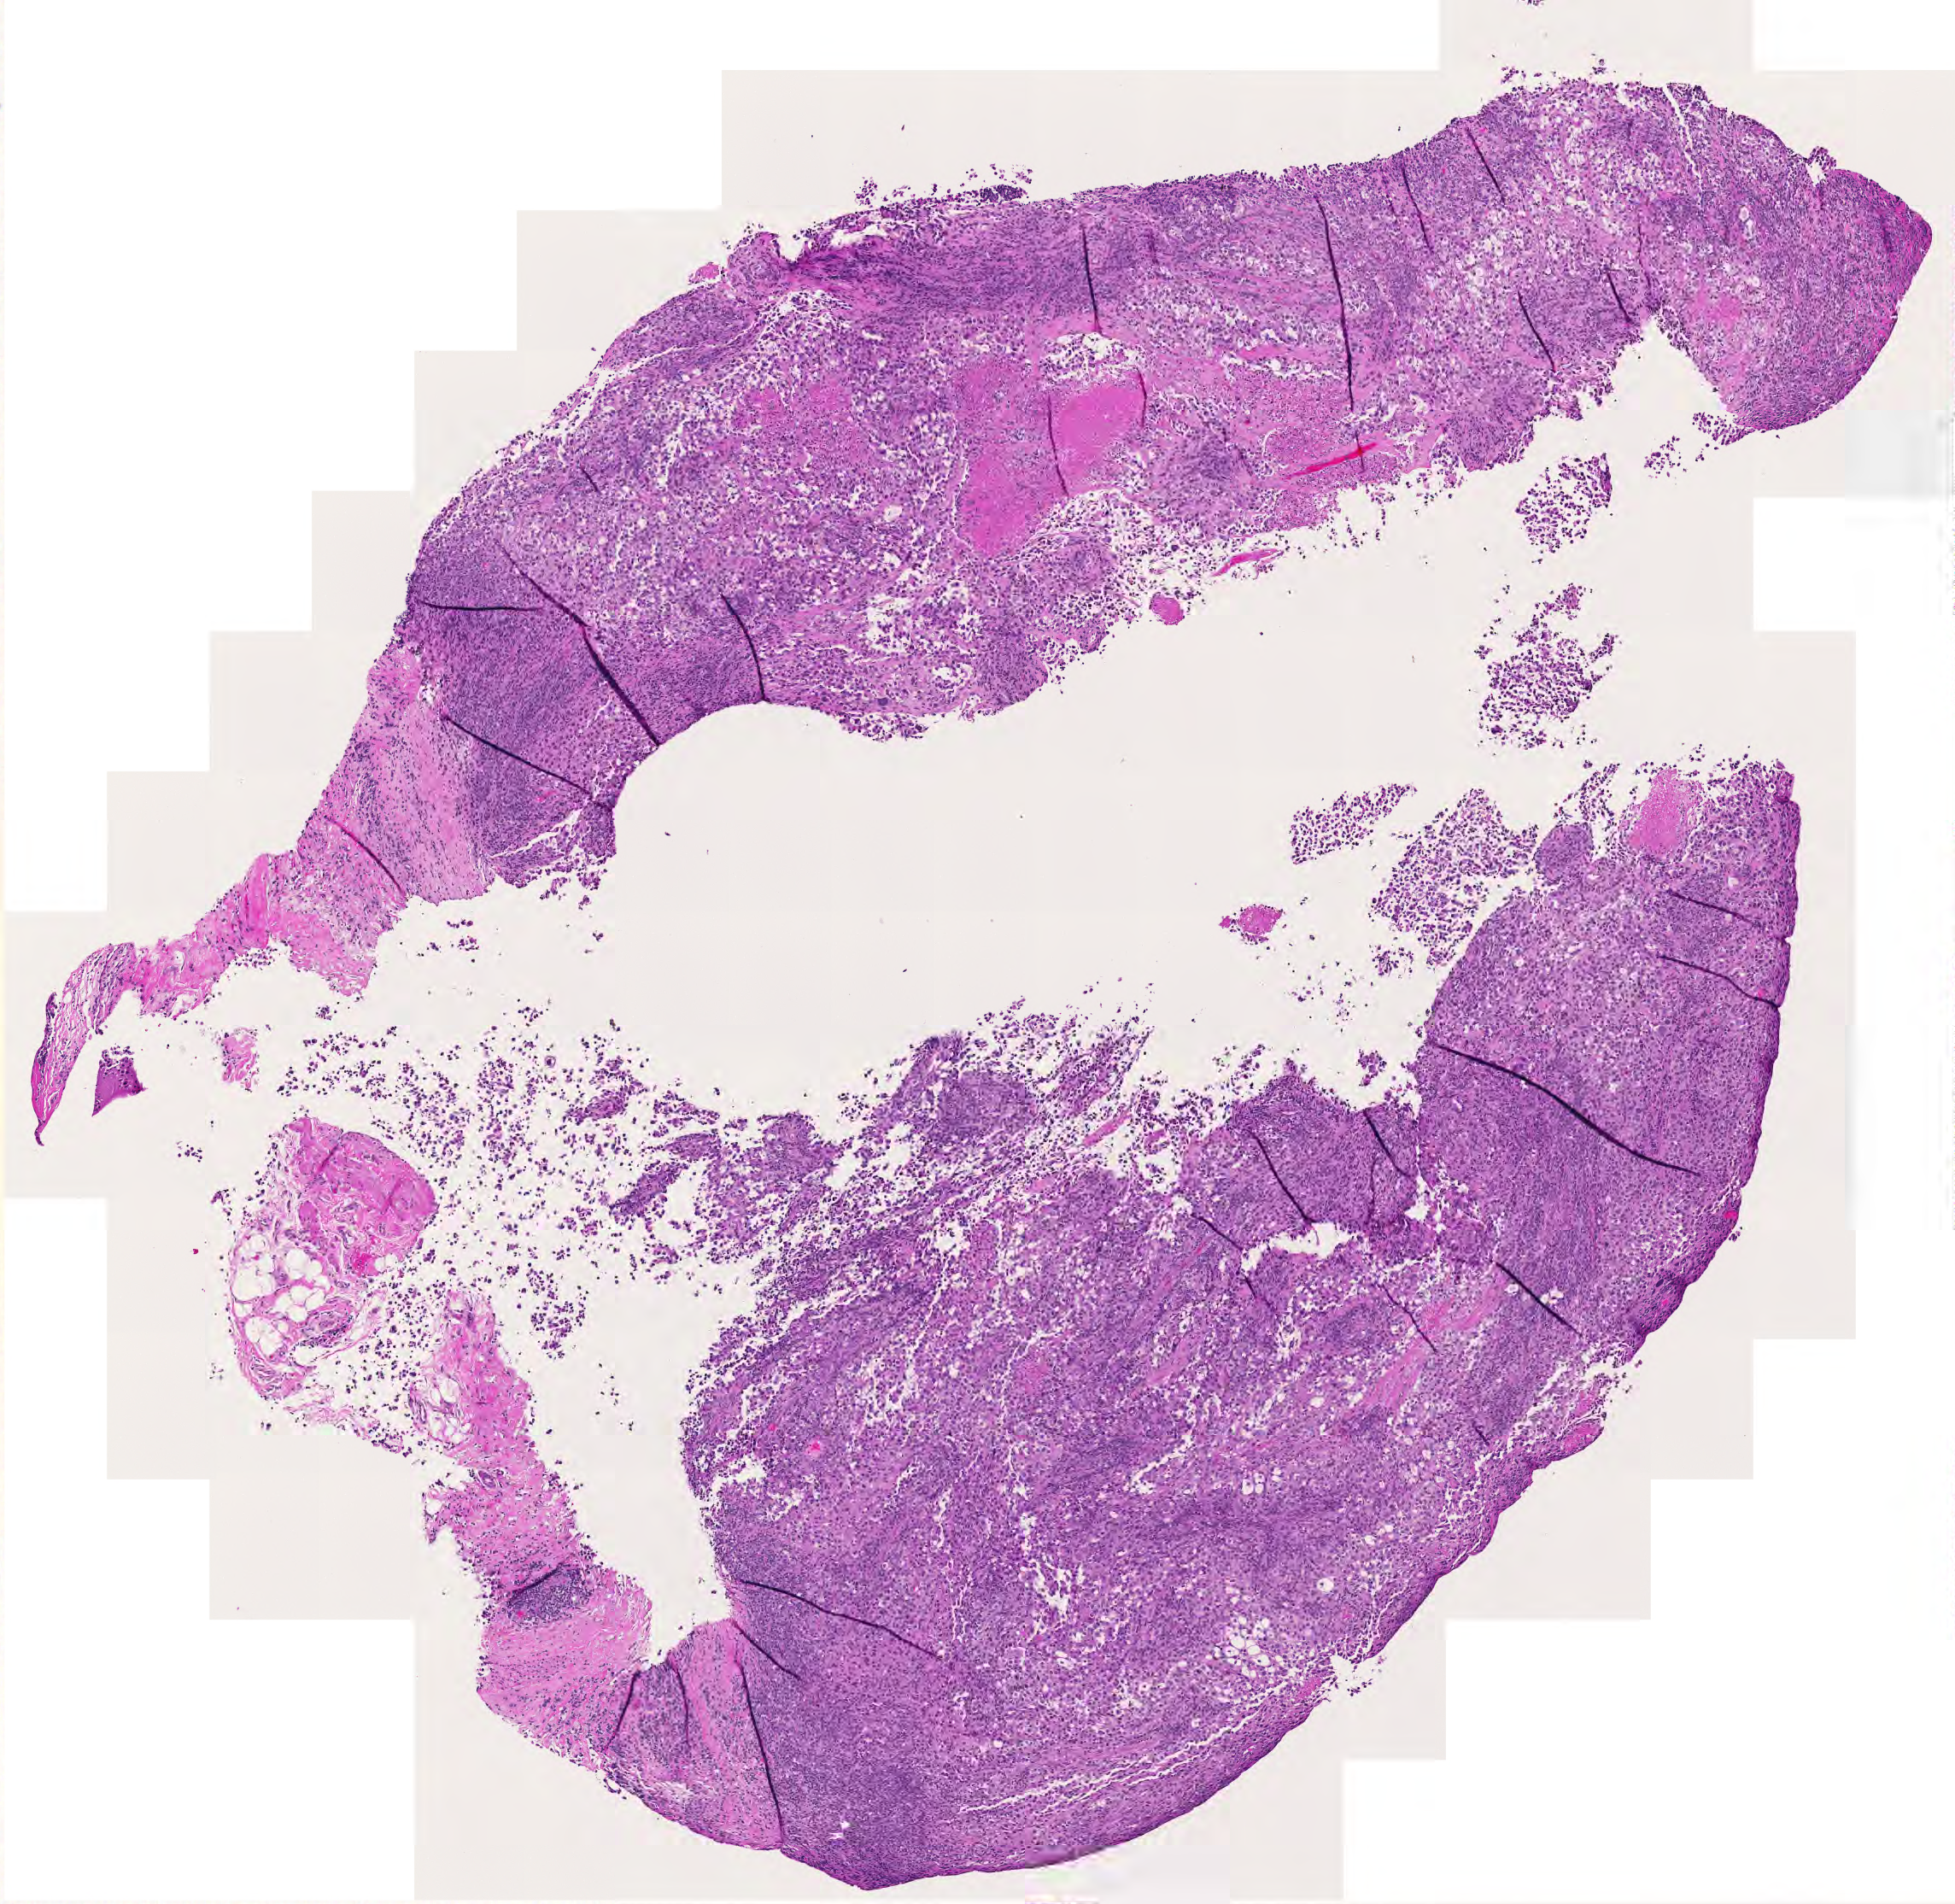
Whole-slide histology image, H&E, low-resolution overview of the scanned area, about 5.9 x 5.8 mm, melanoma tumour tissue; sampled site not recorded. 68-year-old male patient.
AJCC pathologic stage: 0. Diagnosis: Malignant melanoma, NOS.